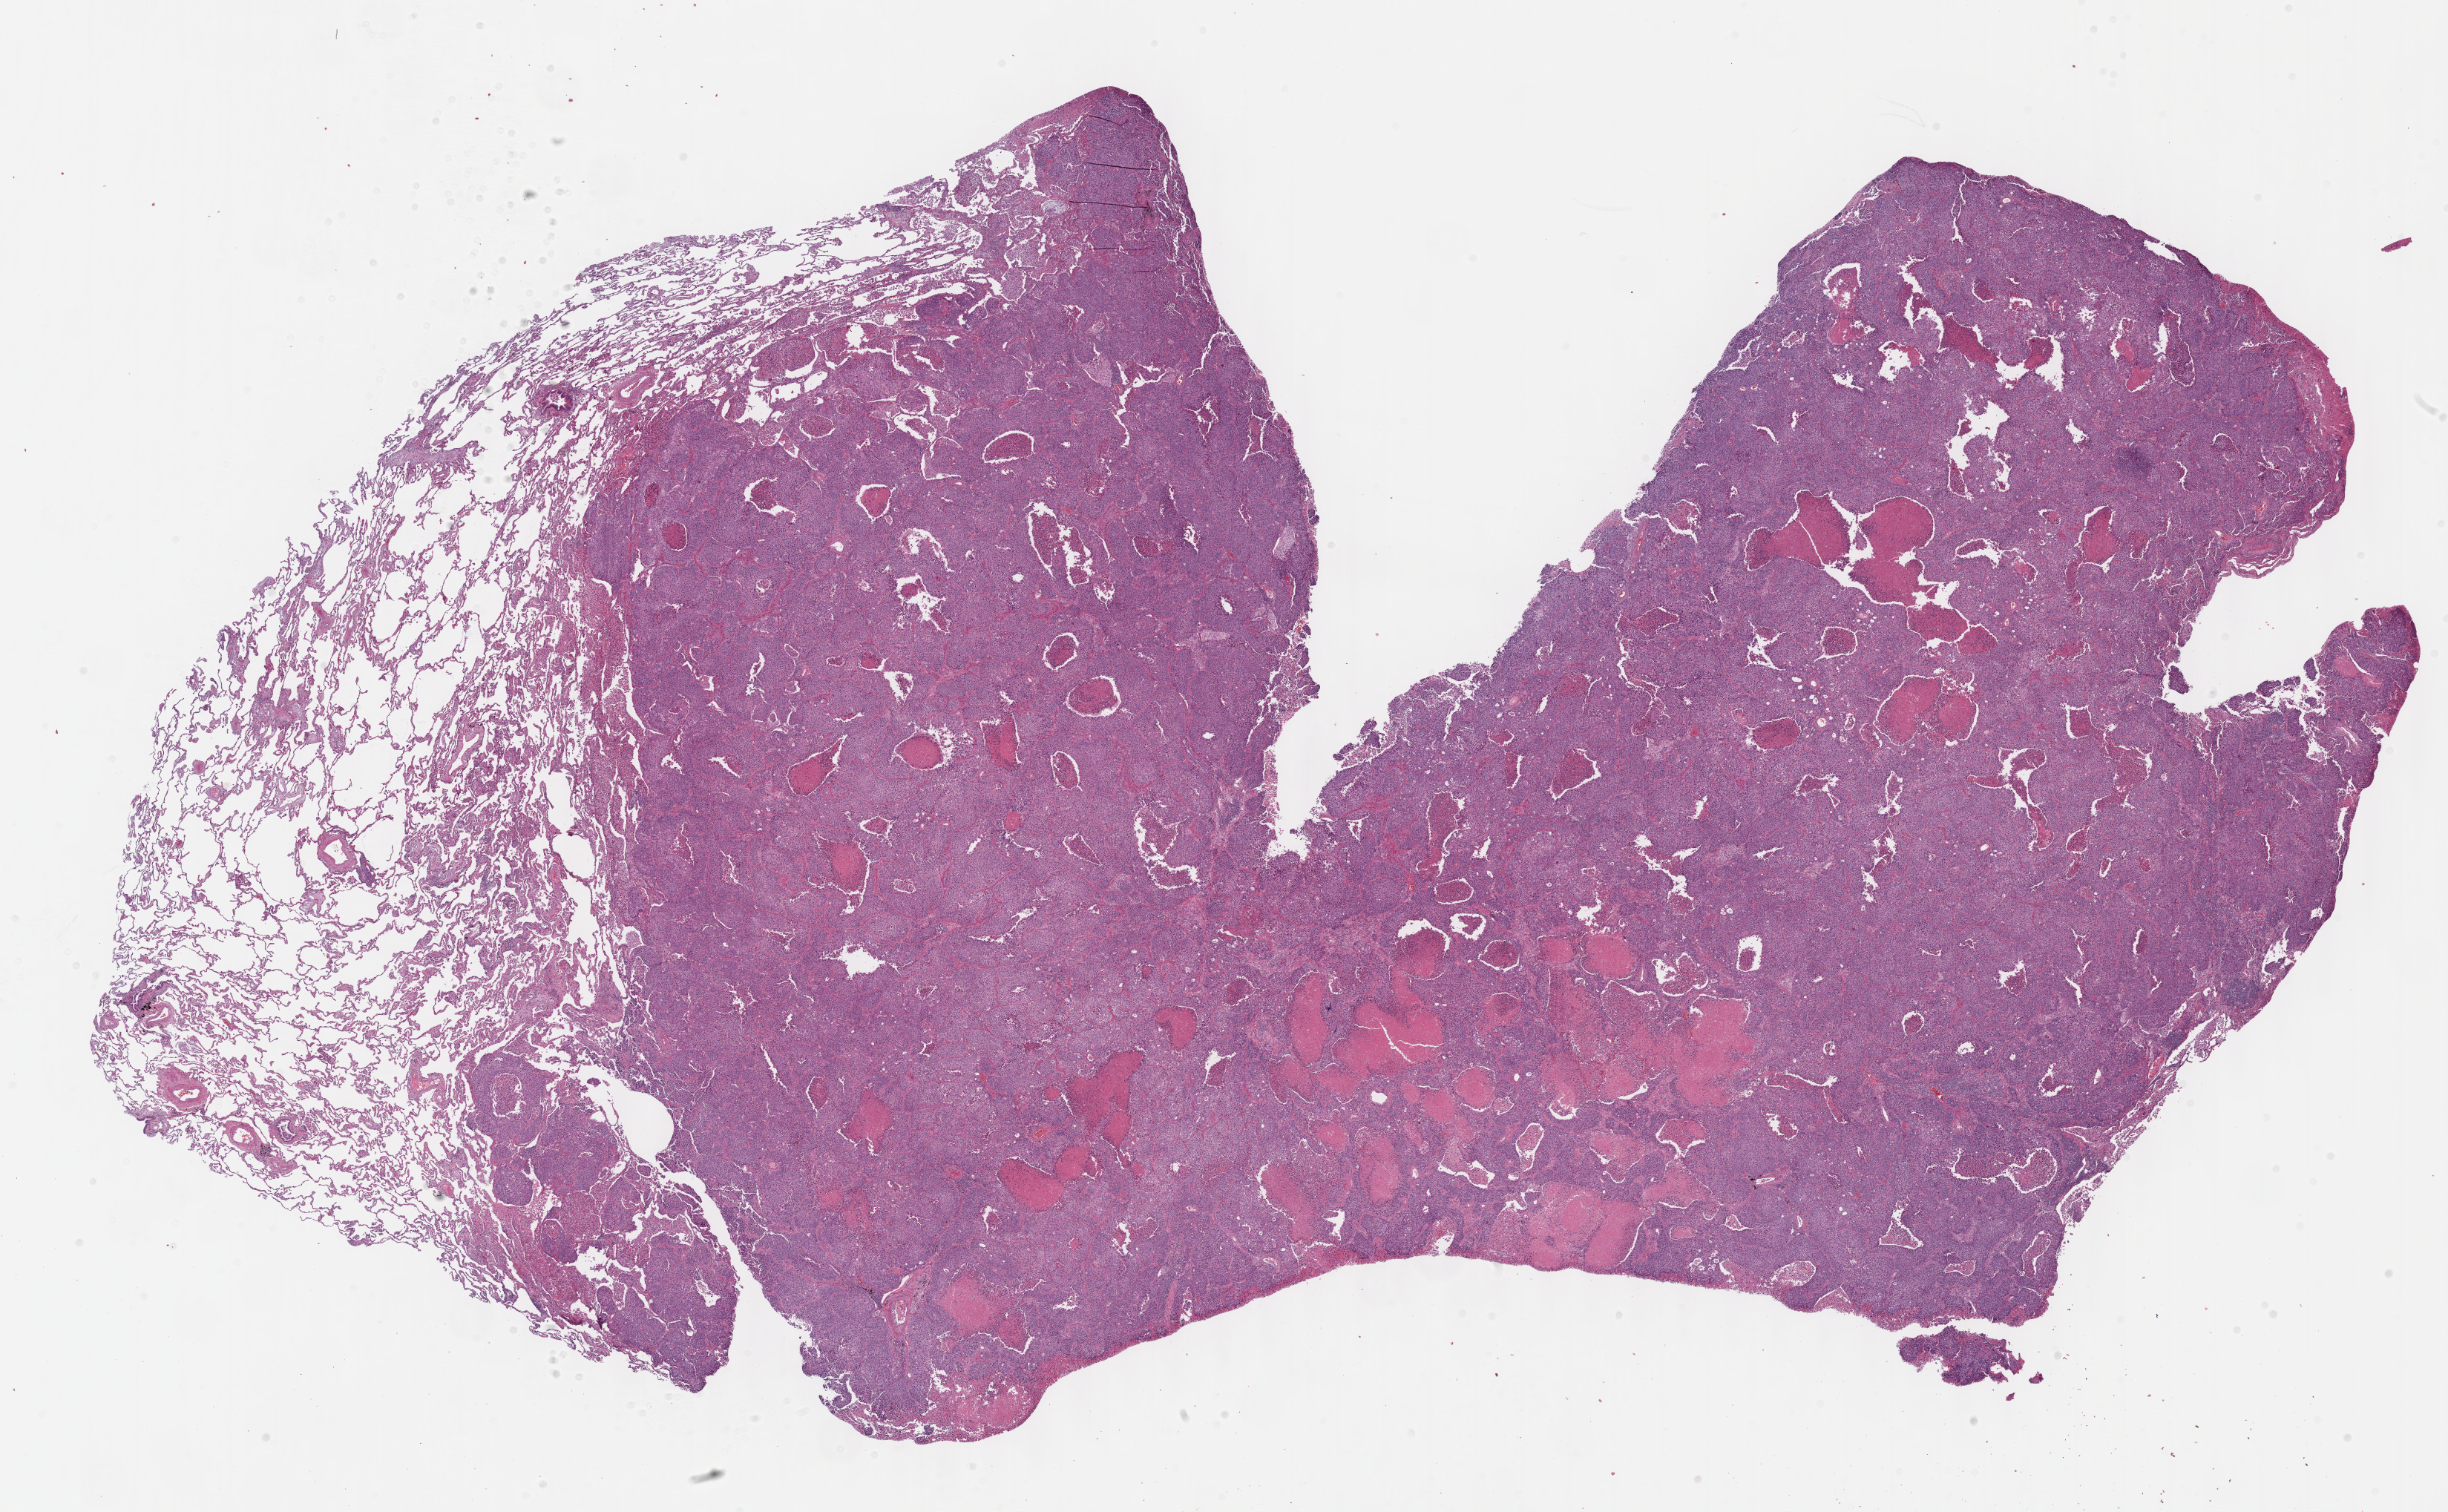
H&E-stained whole-slide image — whole scanned area (about 26.7 x 16.5 mm) shown as a low-resolution overview, formalin-fixed paraffin-embedded (FFPE) diagnostic section, sample: primary tumour, lung. Male patient; age at initial diagnosis 80 years.
AJCC pathologic stage: IIIA. Laterality: right. Diagnosis: Squamous cell carcinoma, NOS (lower lobe, lung).